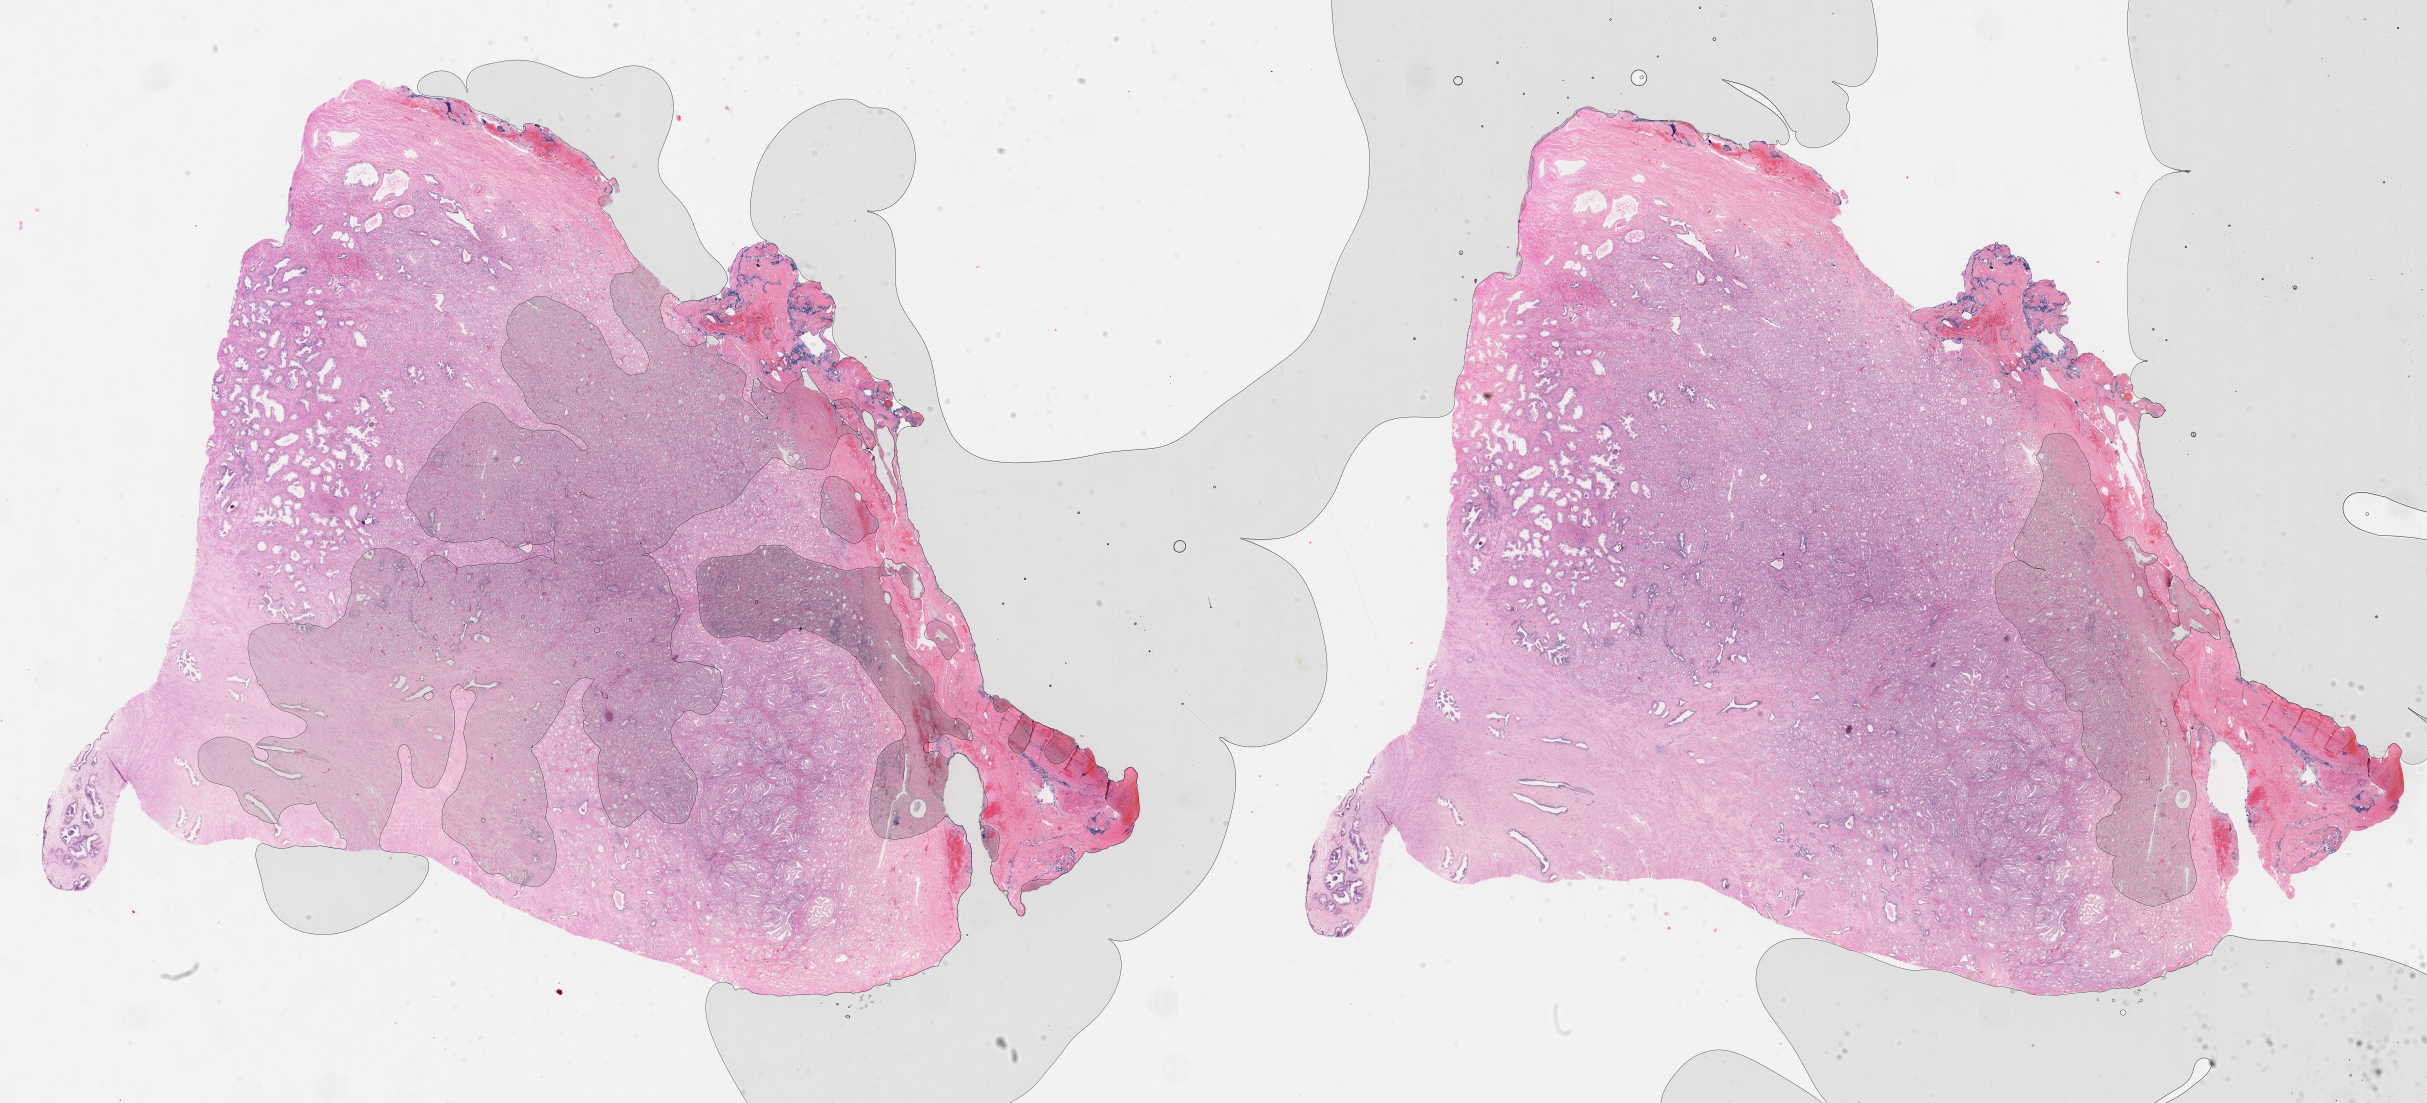
Whole-slide histology image, Hematoxylin and eosin (H&E) stained — whole scanned area (about 39.2 x 17.8 mm, from a 40x scan) shown as a low-resolution overview; formalin-fixed paraffin-embedded (FFPE) diagnostic section; prostate, primary tumour sample. Male patient; age at initial diagnosis 59 years. Gleason score: 7 (3+4).
* laterality: left
* pathologic diagnosis: Adenocarcinoma, NOS (prostate gland)
* lymph nodes positive (case pathology): 0 of 2 examined